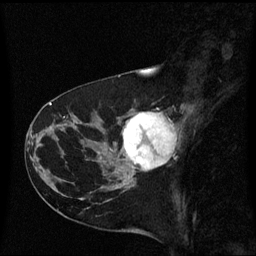
Breast MRI (dynamic contrast-enhanced), one sagittal slice; slice 25 of 60 in the series (ordered by position); dynamic contrast-enhanced series, image 2 of 3 at this slice position (ordered by acquisition); 1.5 T; TE 4.2 ms, TR 8.4 ms; 2 mm slice thickness; 256 × 256 image matrix, field of view 220 × 220 mm. Patient: female, 41 years. From the clinical record (not read from this slice): setting: breast cancer imaged before/during neoadjuvant chemotherapy; receptor status: triple-negative.
Annotated regions visible in this slice (semi-automatically segmented with operator editing):
- analysis volume of interest (the breast-tissue region the enhancement analysis was run in; not a lesion): box from (x=116, y=102) to (x=184, y=177) px
- tumour enhancement mask (voxels above the 70 % enhancement threshold inside the analysis volume of interest): (x=123, y=112)–(x=175, y=171)